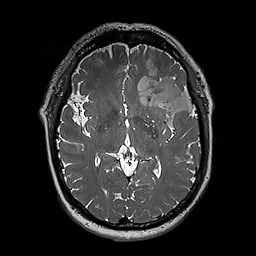
Brain MRI from a brain-tumour surgery series, one axial slice; slice 113 of 192 in the series (ordered by position); 1 mm slice thickness; 256 × 256 image matrix, field of view 250 × 250 mm. From the clinical record (not read from this slice): histopathology: Oligodendroglioma; WHO grade: 3; IDH mutation: yes; tumour location: Left Sylvian Fissure (Temporal).
Annotated regions visible in this slice (manually delineated by an expert):
- tumour: bounding box (x1, y1, x2, y2) in pixels: (124, 57, 197, 126)